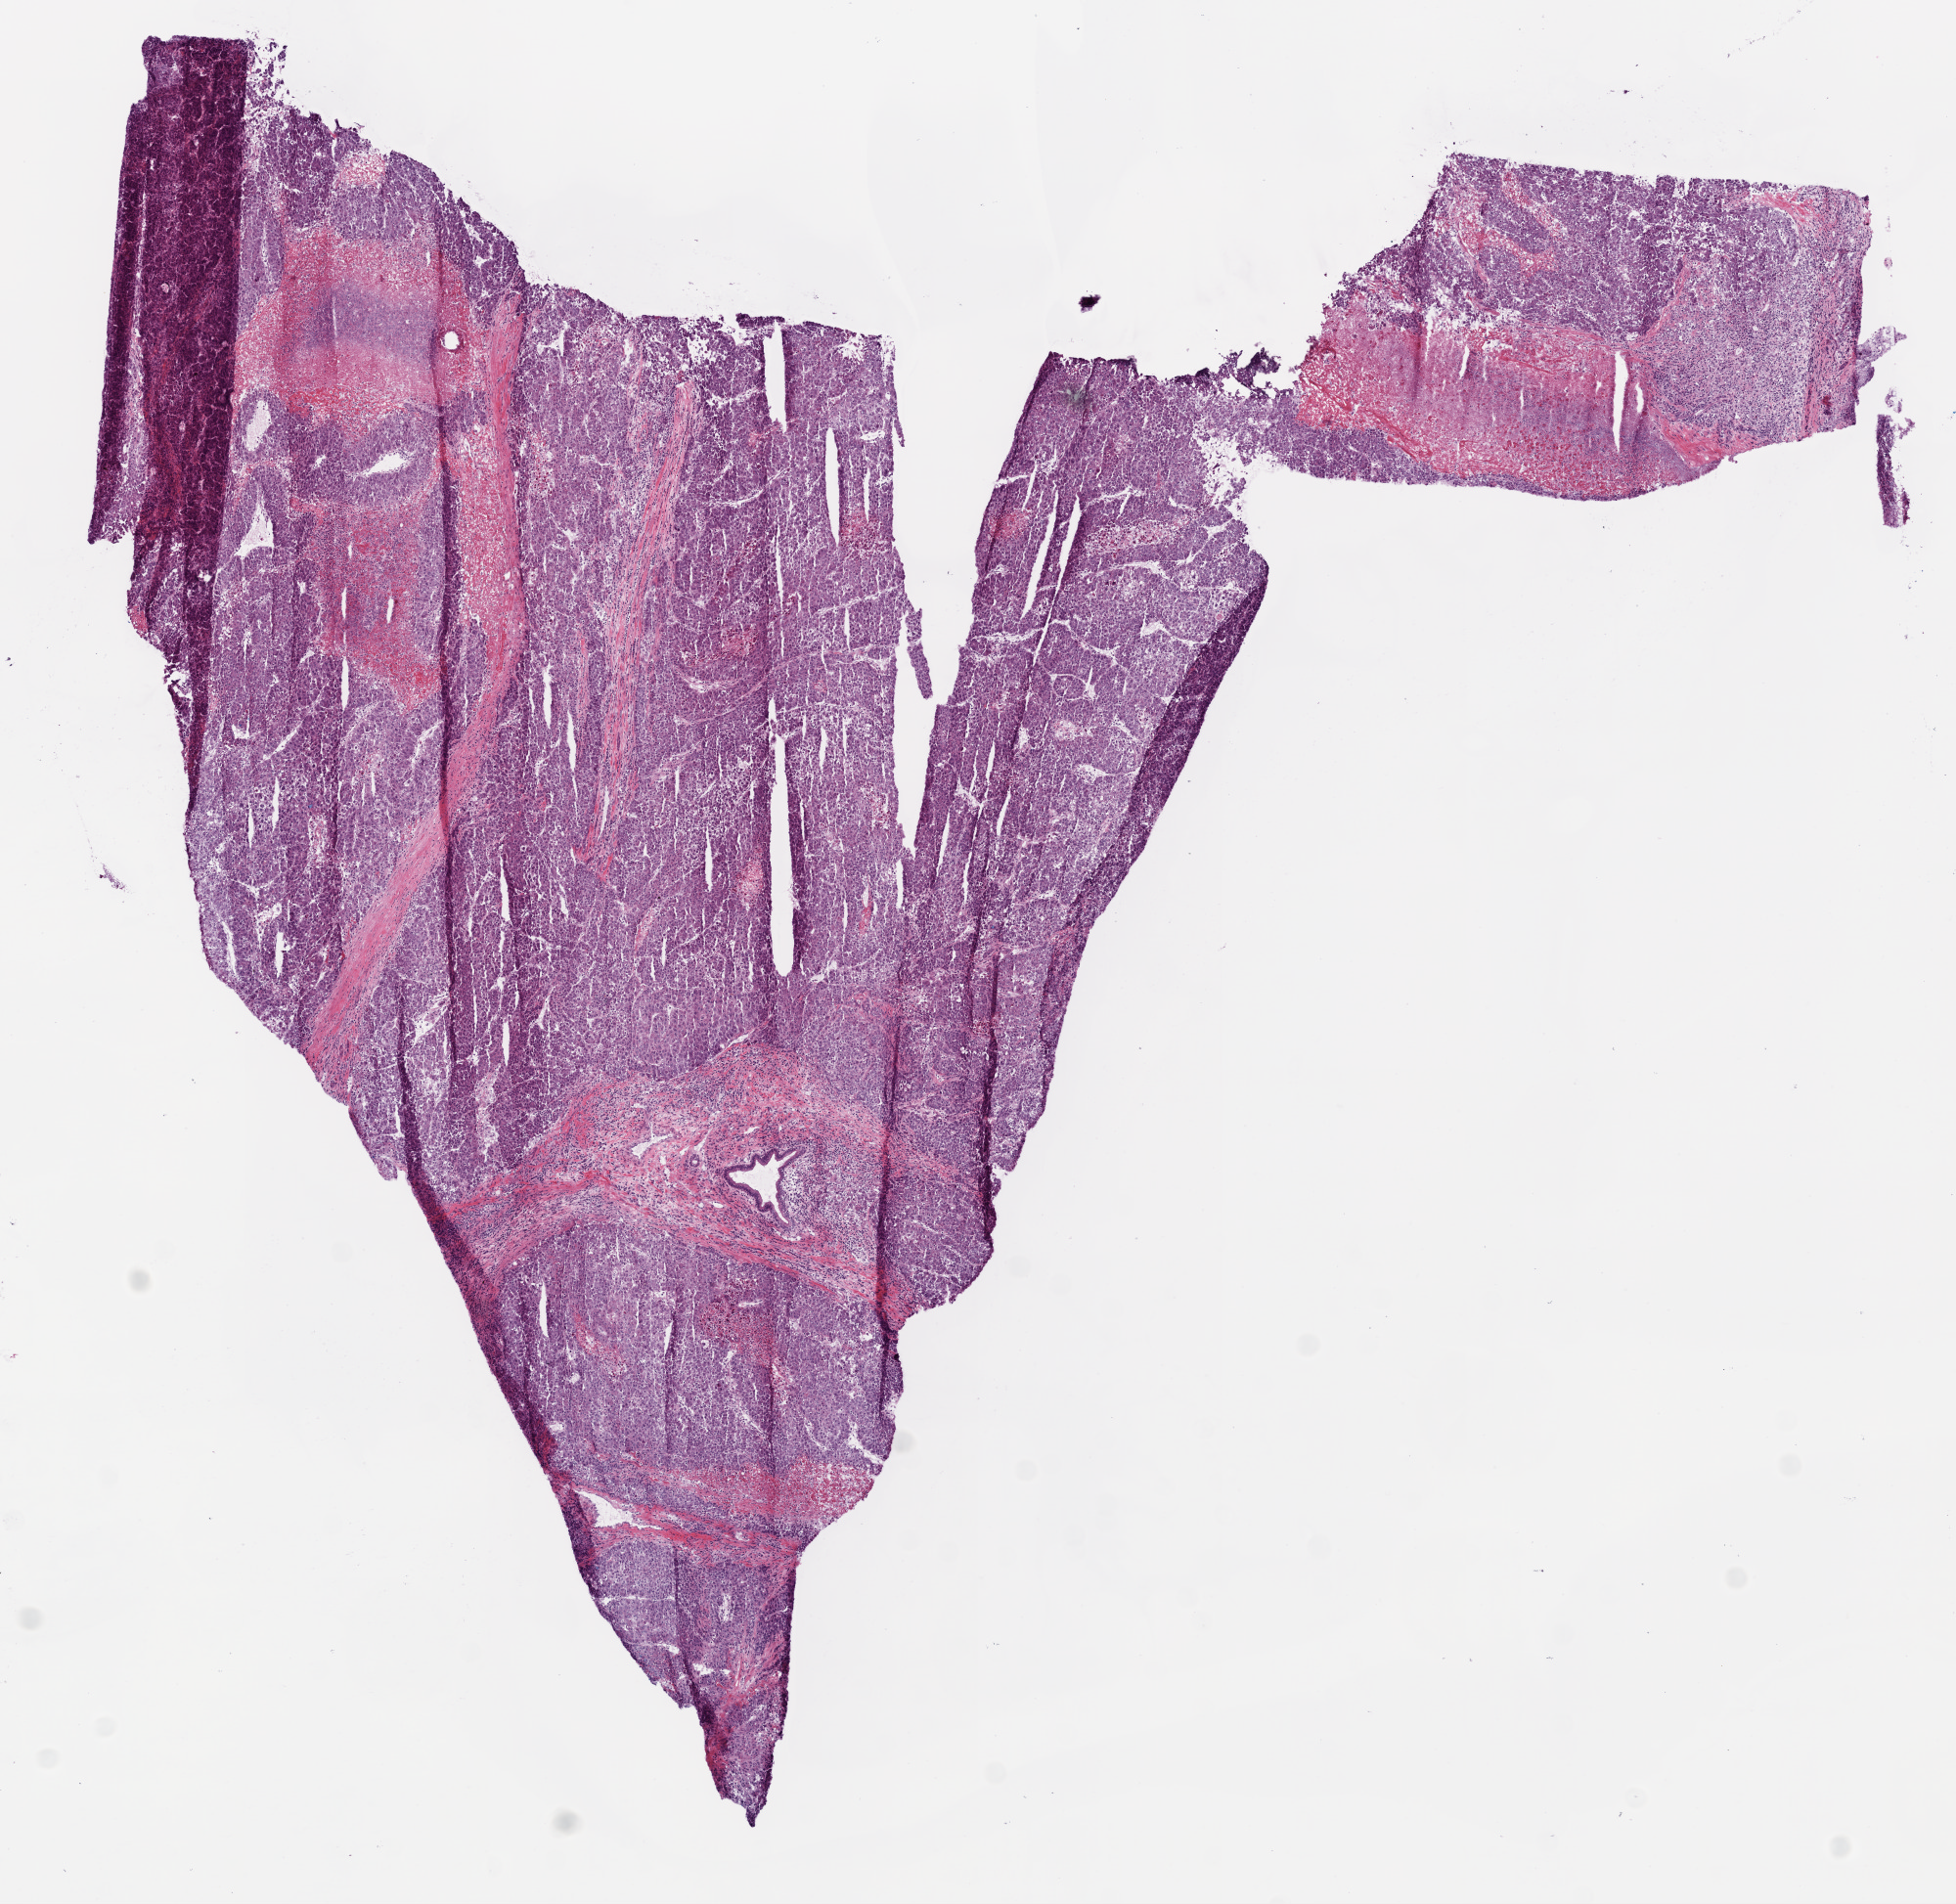
Whole-slide histology image, H&E-stained, low-resolution overview of the scanned area, about 8.0 x 7.8 mm (acquisition: 20x scan); frozen section from the bottom of the tissue portion; sample: primary tumour, liver. Male patient; age at initial diagnosis 73 years. Histologic grade: G3 (poorly differentiated). Pathologist review of this section (percent, as recorded): tumour cells 70%, tumour nuclei 85%, normal cells 0%, stromal cells 10%, necrosis 20%. Infiltration values recorded for this section: lymphocyte infiltration 0%, monocyte infiltration 0%, neutrophil infiltration 0%.
Pathologic diagnosis: Hepatocellular carcinoma, NOS. AJCC pathologic stage: IIIA. TNM: T3 N0 MX.